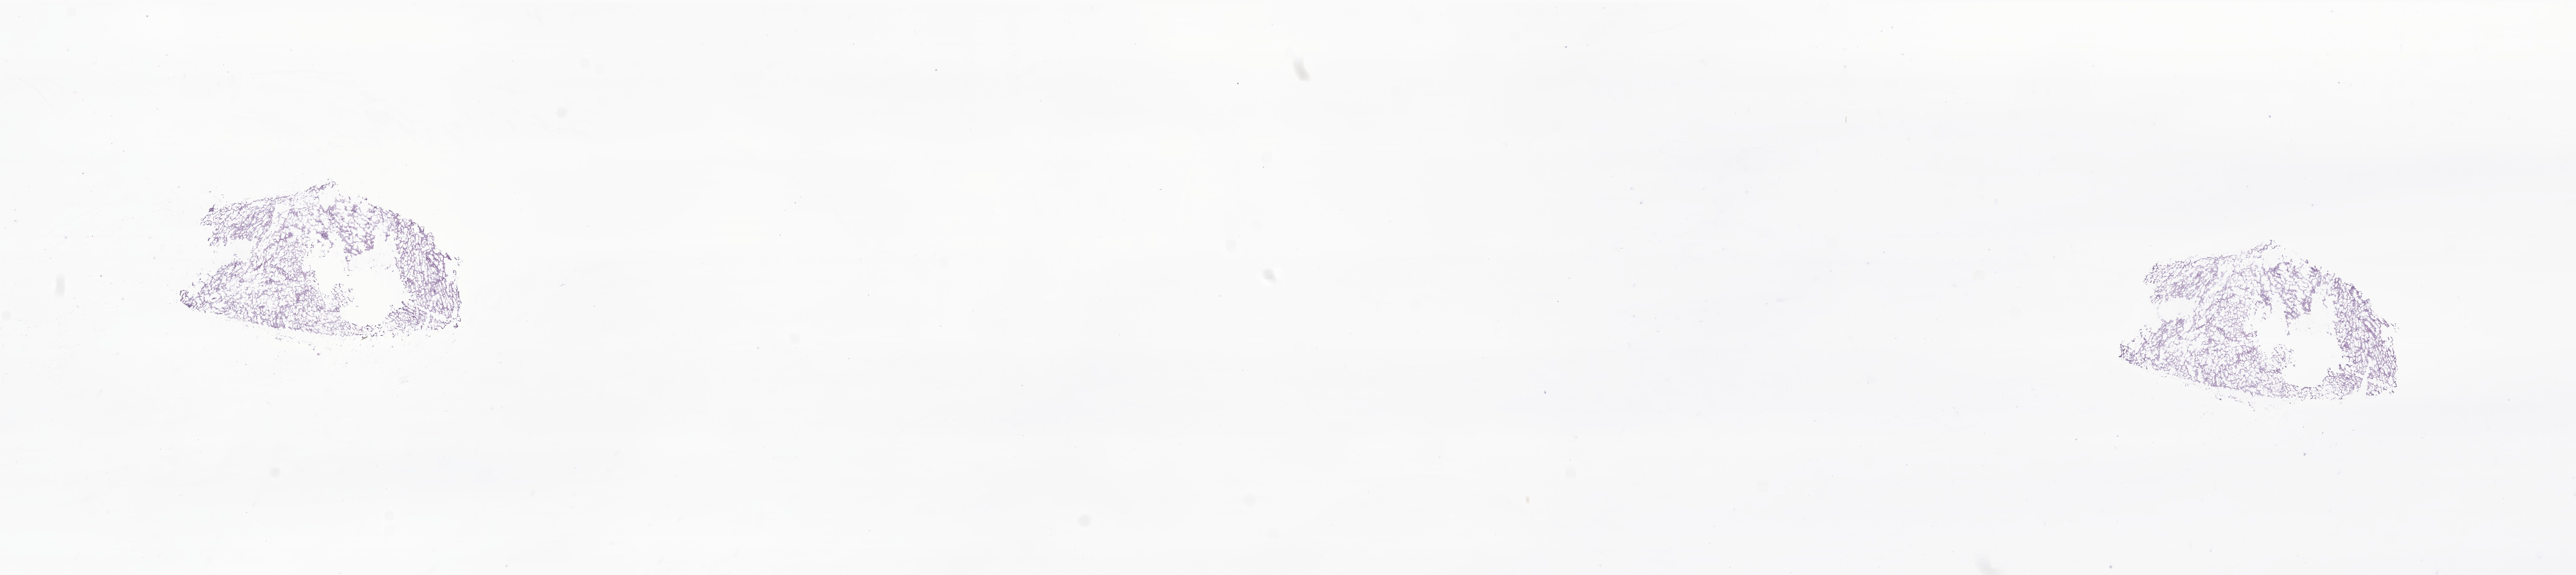
Digitized hematoxylin and eosin (H&E)-stained section of tumor tissue from the brain — a low-resolution overview of the entire scanned area, about 27.7 x 6.2 mm. Cryosection (OCT / tissue freezing medium). Patient male; age 34 months (2 years 10 months).
Recorded diagnosis: Neoplasm, uncertain whether benign or malignant.